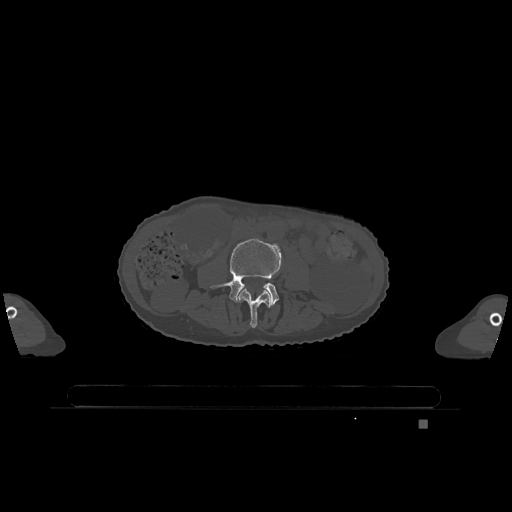
CT including the spine, one axial slice. Bone window (W 1800 / L 400 HU). 0.5 mm slice thickness. 512 × 512 image matrix. Female patient, age 74 years. From the clinical record (not read from this slice): primary cancer: lung.
Annotated regions visible in this slice (semi-automatically segmented with operator editing):
- L3 vertebra: bounding box [x1, y1, x2, y2] px = [238, 288, 271, 328]
- L4 vertebra: [211, 238, 281, 306]